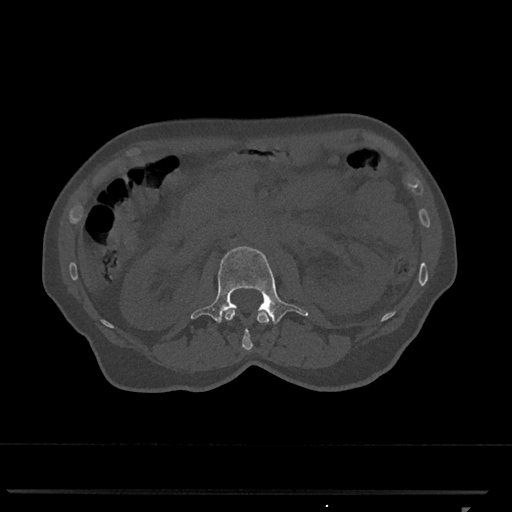
CT including the spine, one axial slice. Position 355 of 793 along the scan axis. Bone window (W 1800 / L 400 HU). 0.5 mm slice thickness. 512 × 512 image matrix, field of view 380 × 380 mm. Patient: female, 62 years. From the clinical record (not read from this slice): primary cancer: renal.
Structures marked on this image (semi-automatically segmented with operator editing):
- L1 vertebra: bounding box (x1, y1, x2, y2) in pixels: (225, 309, 270, 351)
- L2 vertebra: (190, 246, 308, 324)